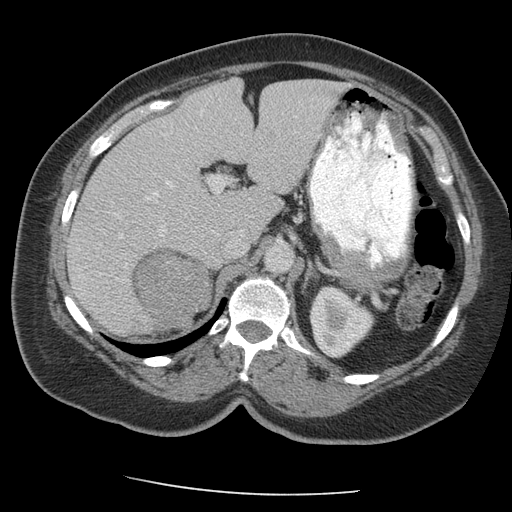
Contrast-enhanced abdominal CT, one axial slice; position 128 of 163 along the scan axis; 140 kVp; intravenous contrast given; soft-tissue window (W 400 / L 40 HU); 2.5 mm slice thickness; 512 × 512 image matrix, field of view 360 × 360 mm. Patient: female, 70 years. From the clinical record (not read from this slice): diagnosis: adrenocortical carcinoma; tumour side: right adrenal.
Outlined on this slice (semi-automatically segmented with operator editing):
- mass: bounding box (x1, y1, x2, y2) in pixels: (135, 252, 211, 332)